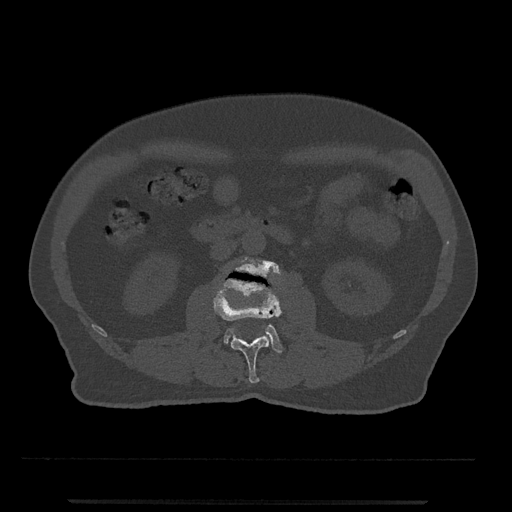
CT including the spine, one axial slice; position 243 of 797 along the scan axis; reconstruction kernel Br40s/3; 120 kVp; bone window (W 1800 / L 400 HU); 0.5 mm slice thickness; 512 × 512 image matrix. Male patient, age 63 years. Case-level facts recorded for this patient, not image findings: primary cancer: prostate.
Annotated regions visible in this slice (semi-automatic segmentation, software-assisted and operator-edited):
- L2 vertebra: box from (x=213, y=279) to (x=282, y=383) px
- L3 vertebra: (x=224, y=257)–(x=283, y=353)